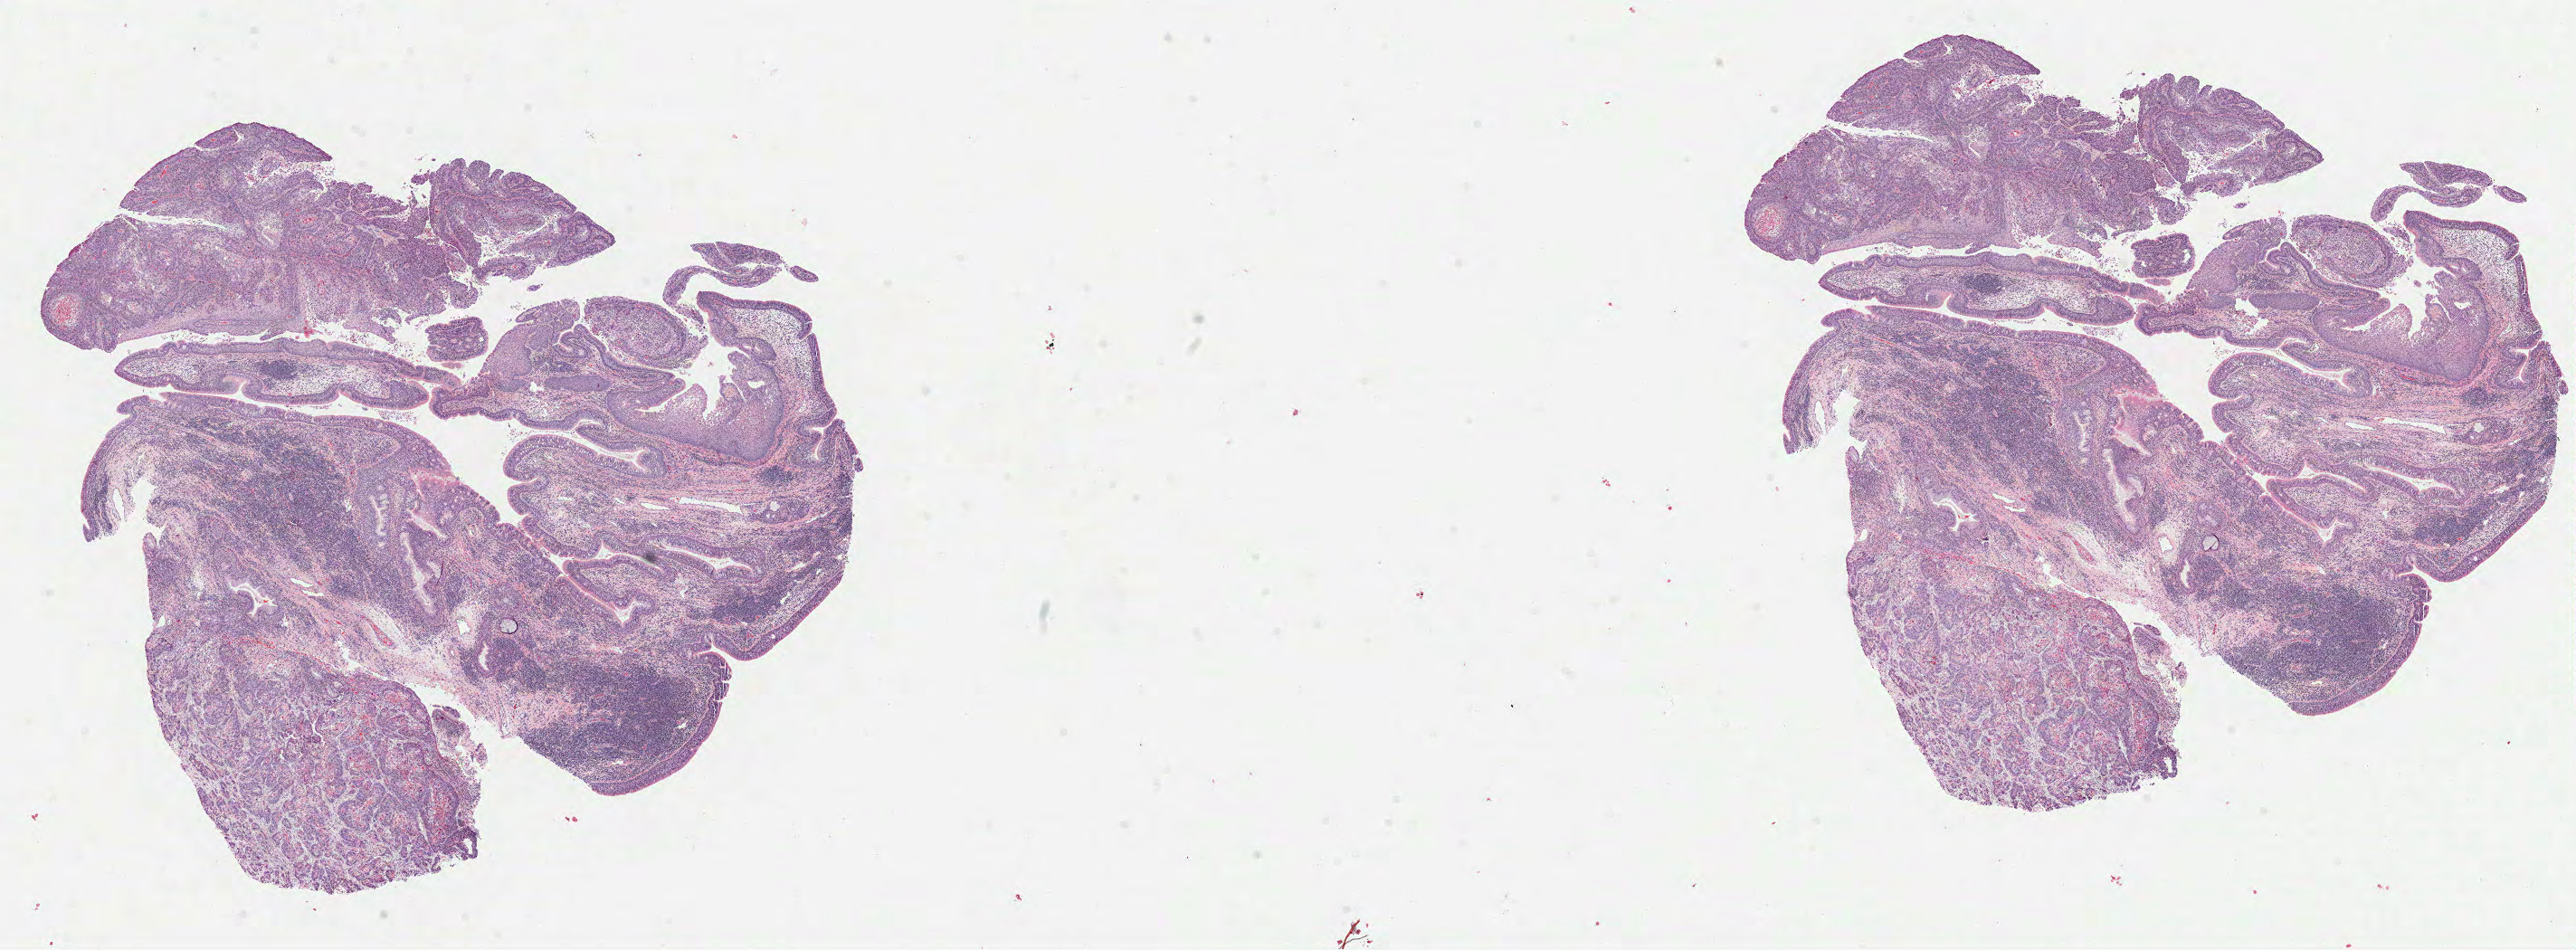
Hematoxylin and eosin (H&E) stained whole-slide image, a low-resolution overview of the entire scanned area, about 23.0 x 8.5 mm (slide scanned at 40x), formalin-fixed paraffin-embedded (FFPE) diagnostic section, head and neck, primary tumour sample. Male, age 47 years at initial diagnosis. Histologic grade: G3 (poorly differentiated).
Histologic diagnosis: Squamous cell carcinoma, NOS (larynx, NOS). AJCC pathologic stage: IVA (7th edition).